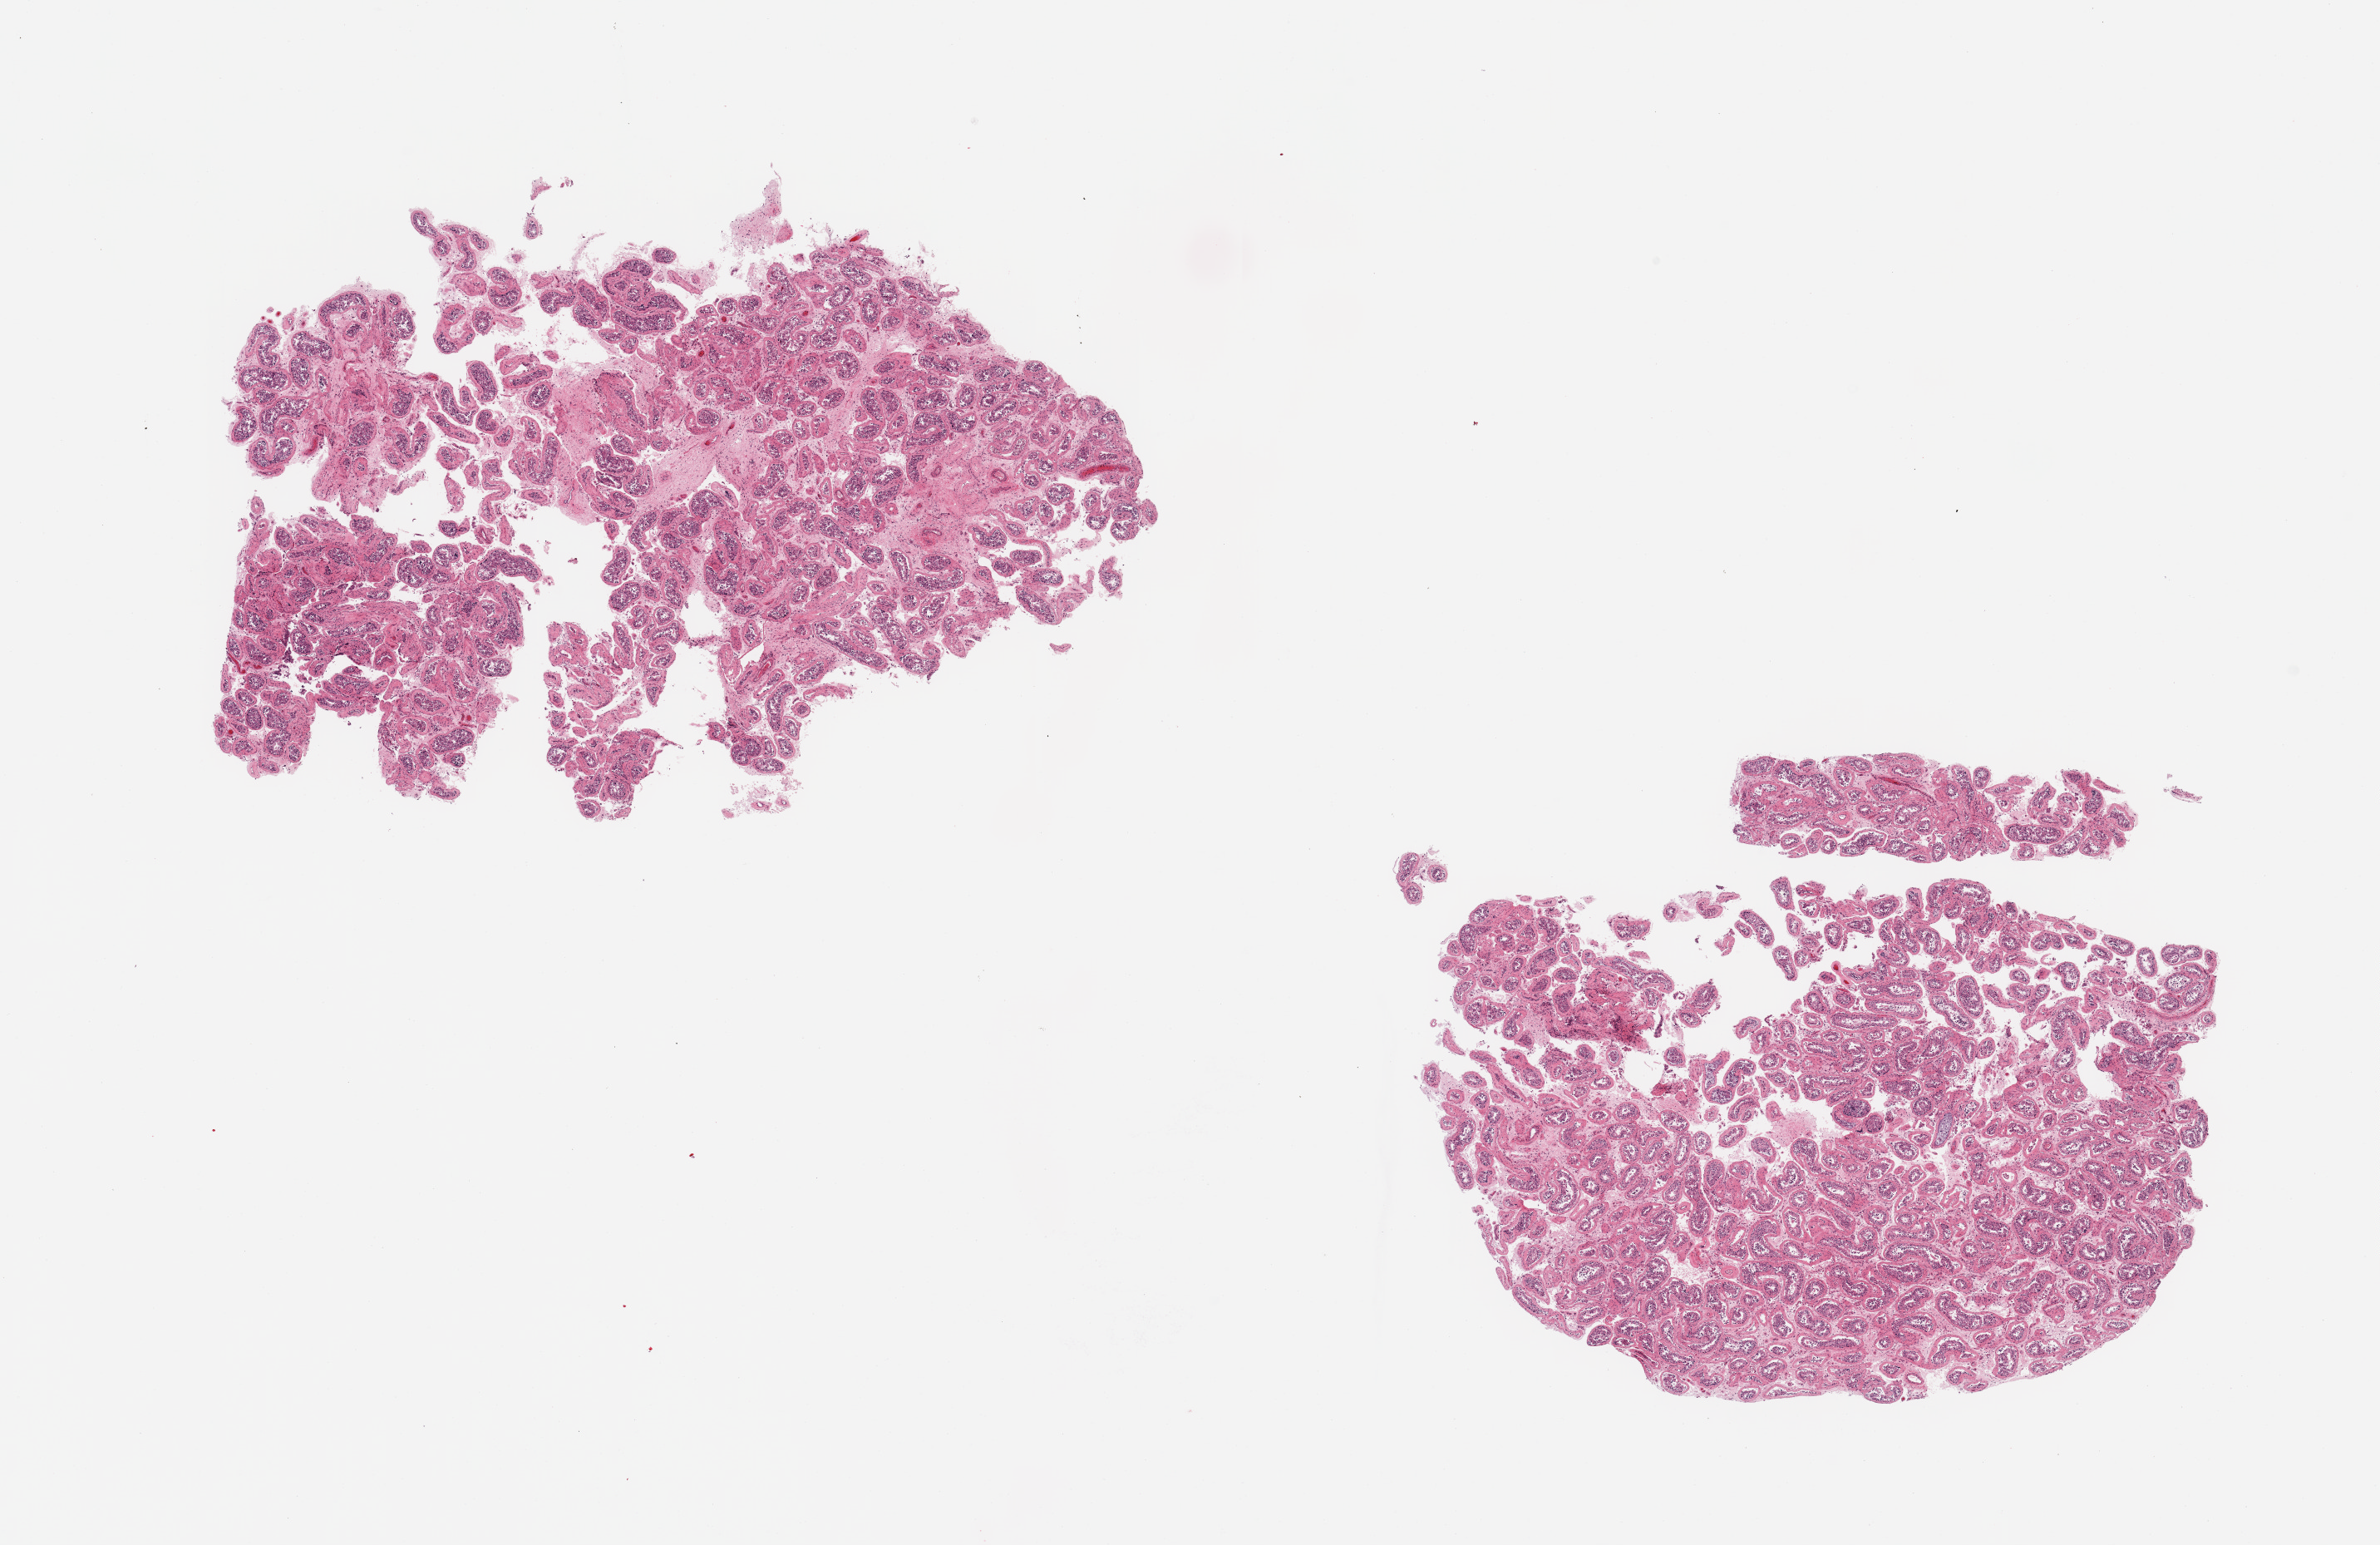
Whole-slide image, hematoxylin and eosin (H&E) stain, brightfield — a low-resolution overview of the entire scanned area, about 22.6 x 14.7 mm. PAXgene-fixed, paraffin-embedded tissue. Section of testis (target tissue). Donor tissue sample. Male donor.
* review note (as recorded): 2 pieces; some tubular hyalinization and reduced/absent spermatogenesis